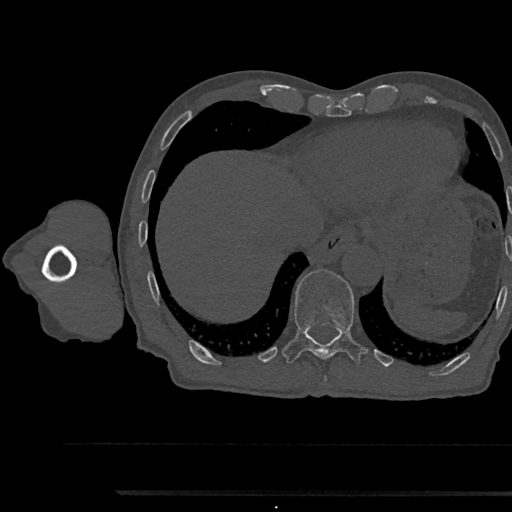
CT including the spine, one axial slice. Position 793 of 797 along the scan axis. Reconstruction kernel Br40s/3. Bone window (W 1800 / L 400 HU). 512 × 512 image matrix. Patient: male, 79 years. From the clinical record (not read from this slice): primary cancer: prostate.
Outlined on this slice (semi-automatically segmented with operator editing):
- T11 vertebra: box from (x=282, y=270) to (x=367, y=363) px